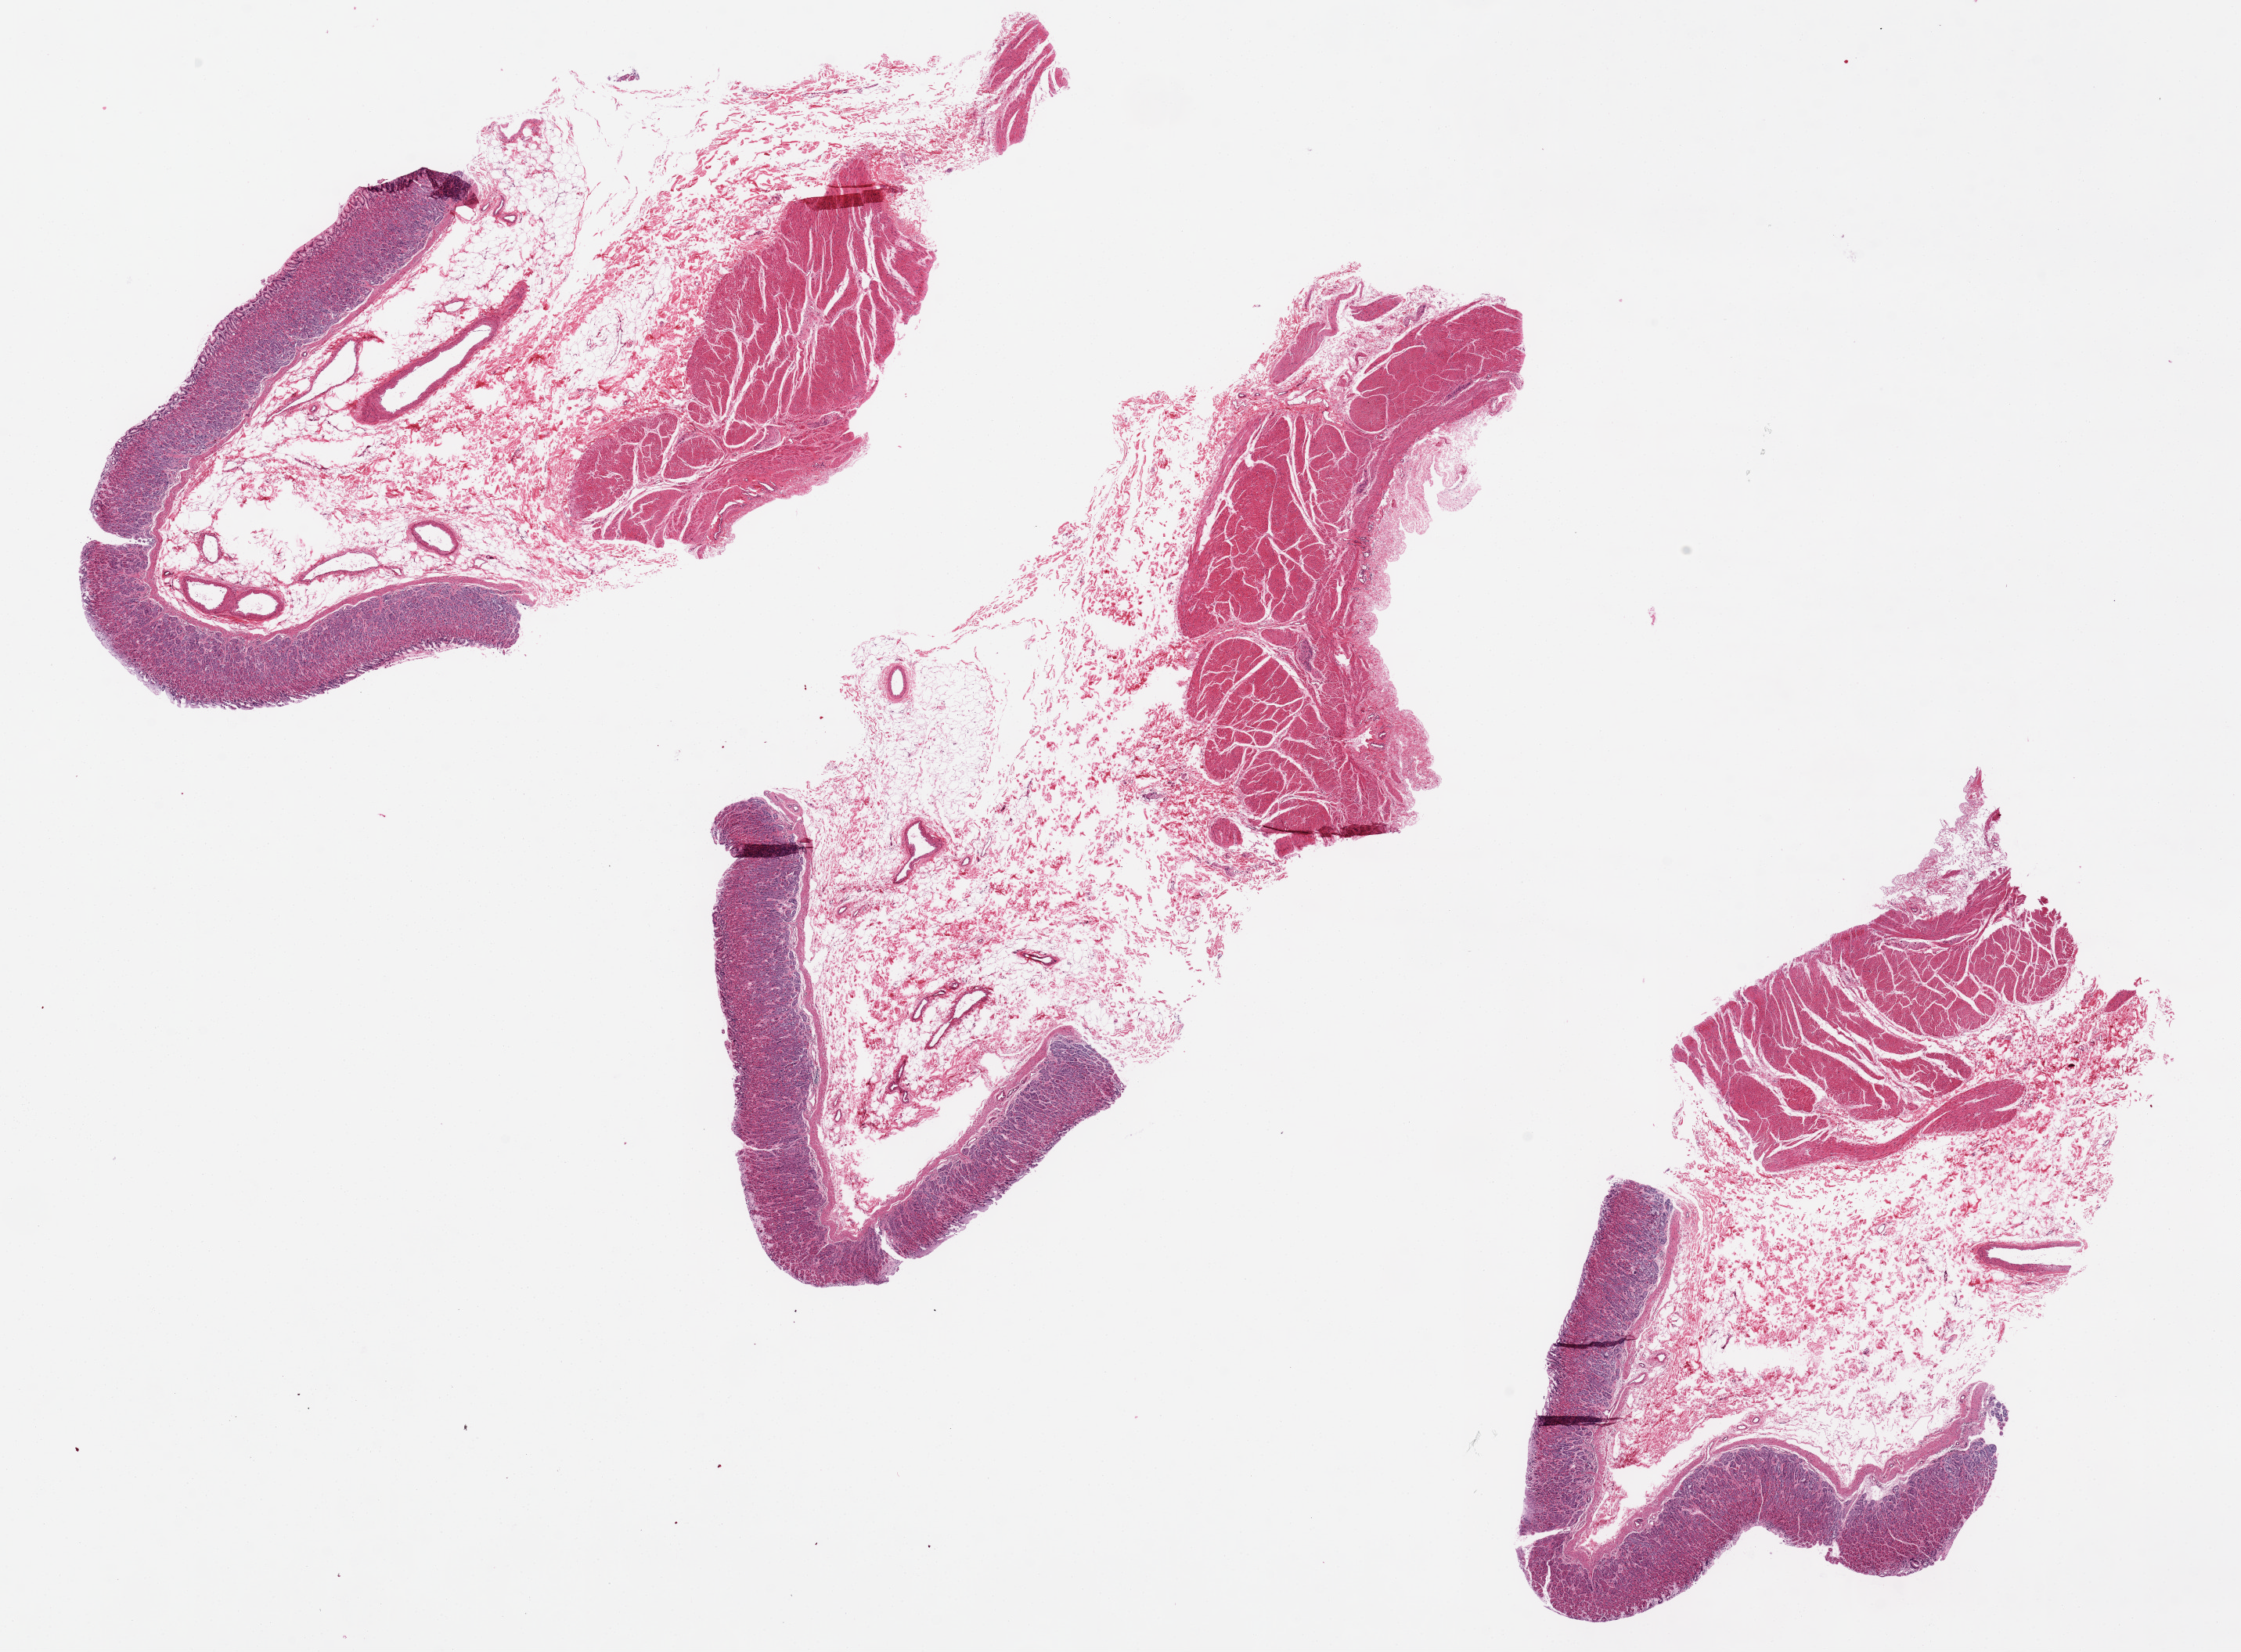
Digitized H&E-stained section, brightfield, shown as a low-resolution overview of the whole scanned area (about 22.6 x 16.7 mm). PAXgene-fixed, paraffin-embedded tissue. Target tissue: stomach. Tissue donor sample. Male donor.
Reviewer comment on this tissue sample: Deep glands OK; surface autolyzed.